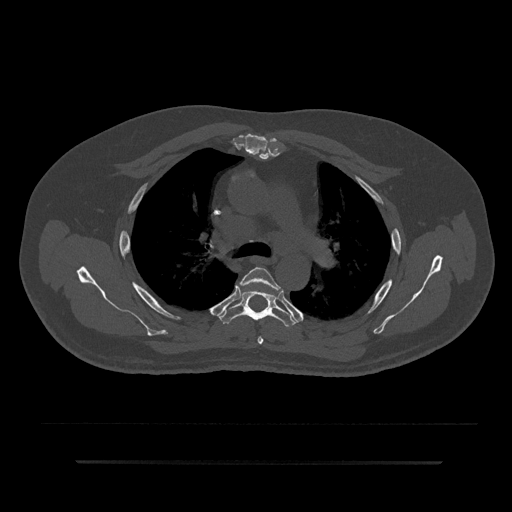
CT including the spine, one axial slice. Position 589 of 797 along the scan axis. Reconstruction kernel Br40s/3. Bone window (W 1800 / L 400 HU). 0.5 mm slice thickness. 512 × 512 image matrix, field of view 464 × 464 mm. Patient: male, 59 years. From the clinical record (not read from this slice): primary cancer: bile ducts; vertebrae with lytic lesions (as recorded): T10.
Outlined on this slice (semi-automatic segmentation, software-assisted and operator-edited):
- T4 vertebra: bounding box [x1, y1, x2, y2] px = [240, 267, 281, 345]
- T5 vertebra: [219, 290, 297, 327]